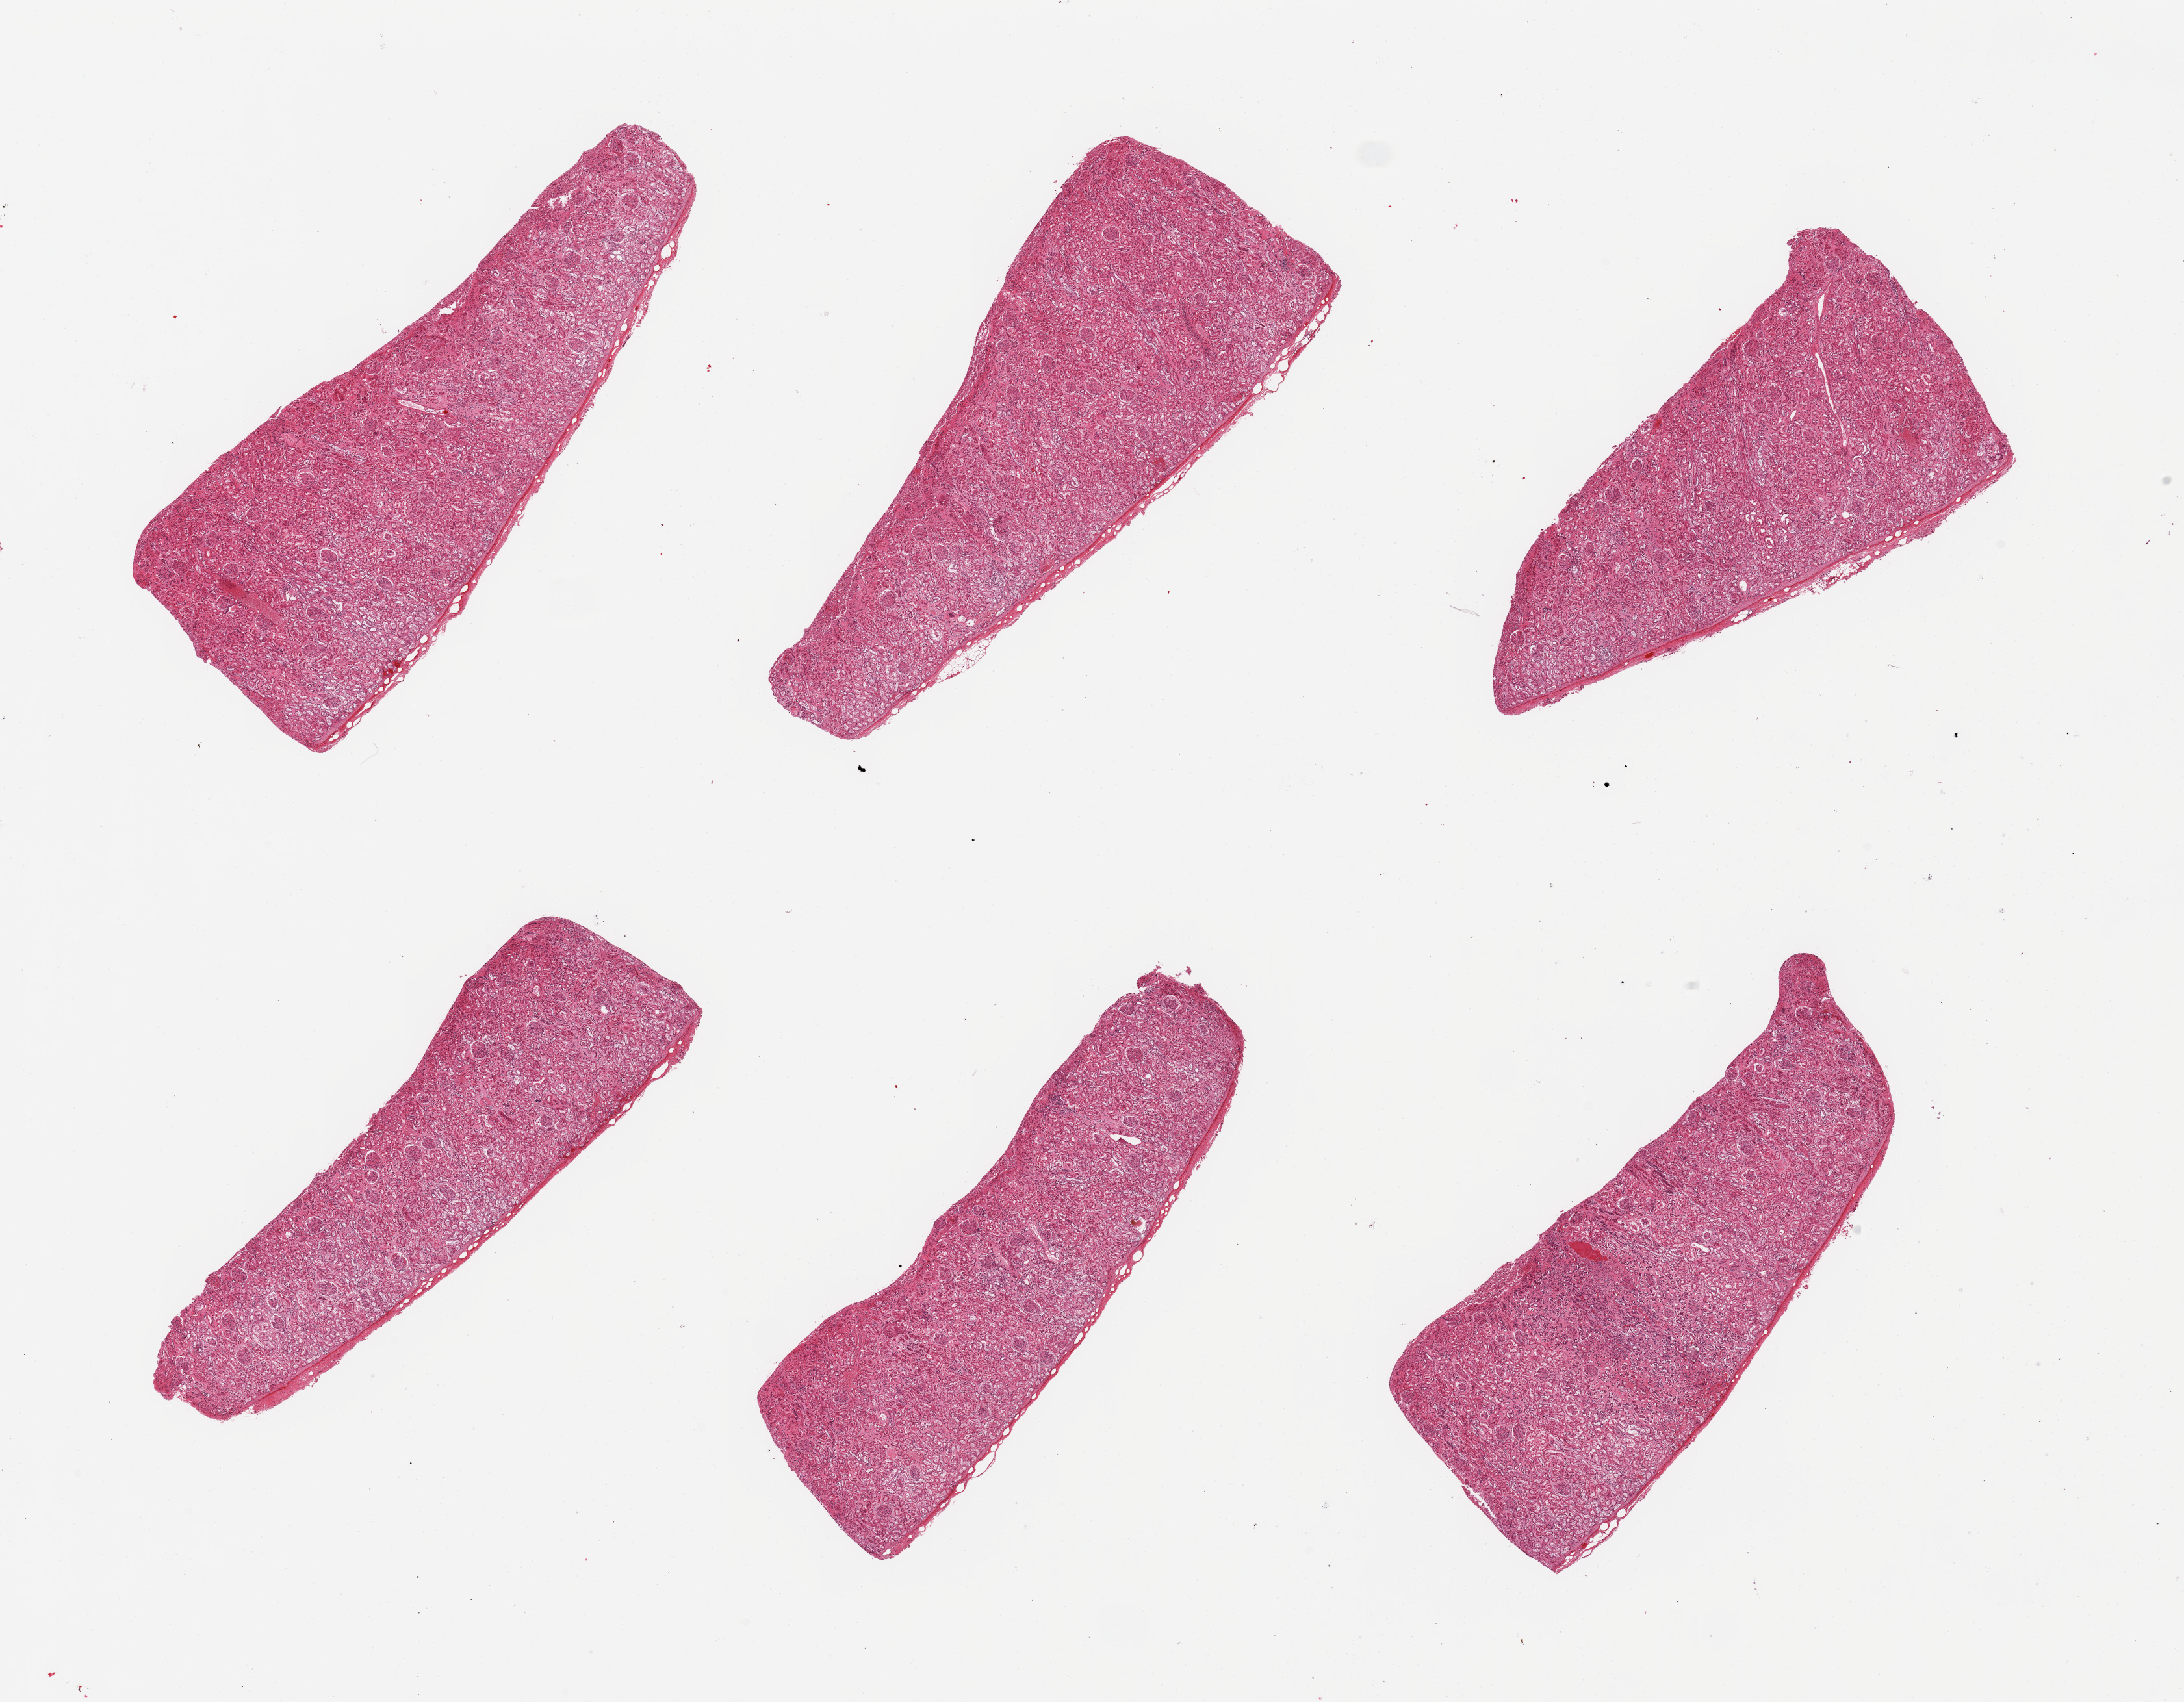
Haematoxylin and eosin whole-slide image, a low-resolution overview of the entire scanned area, about 26.6 x 20.7 mm; PAXgene-fixed, paraffin-embedded tissue; sampled site (target tissue): renal cortex; donor tissue sample. Male donor.
- review note (as recorded): 6 pieces; glomeruli present in all sections